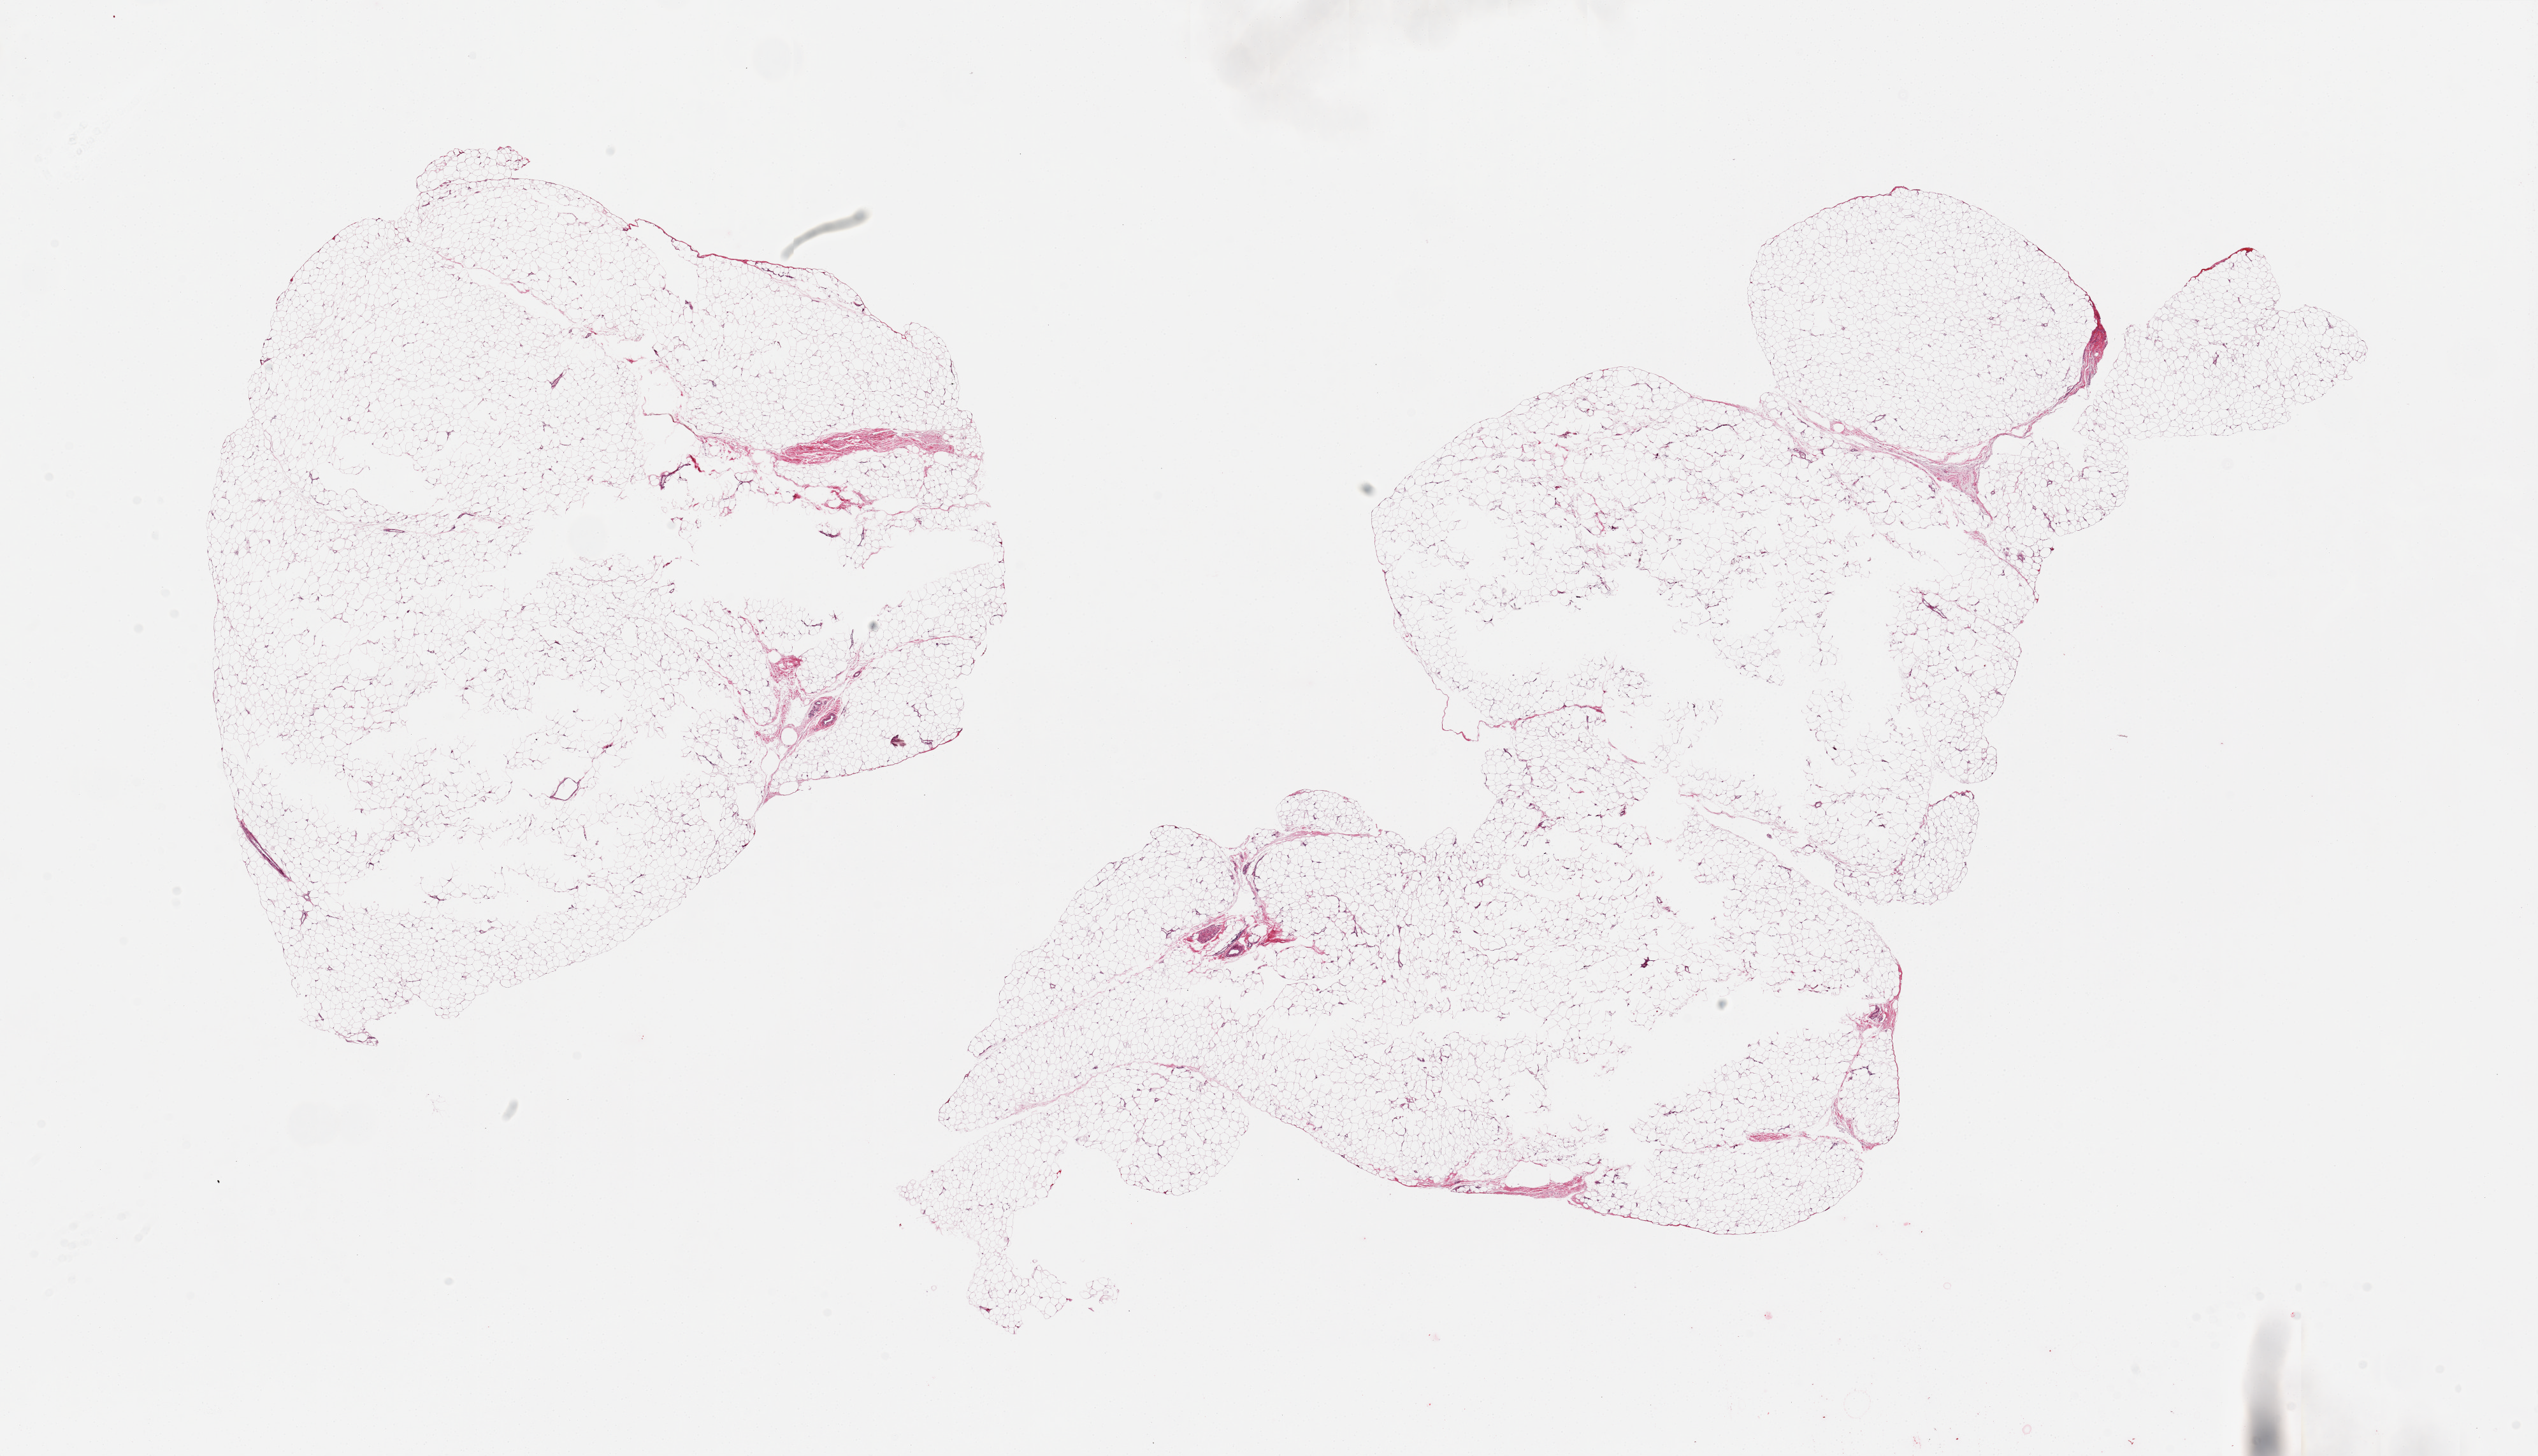
Digitized hematoxylin and eosin (H&E)-stained section, brightfield — a low-resolution overview of the entire scanned area, about 31.5 x 18.1 mm, PAXgene-fixed, paraffin-embedded tissue, target tissue: adipose tissue, donor tissue sample. Male donor.
- review note (as recorded): 2 pieces, 11x10 and 18x8.5mm